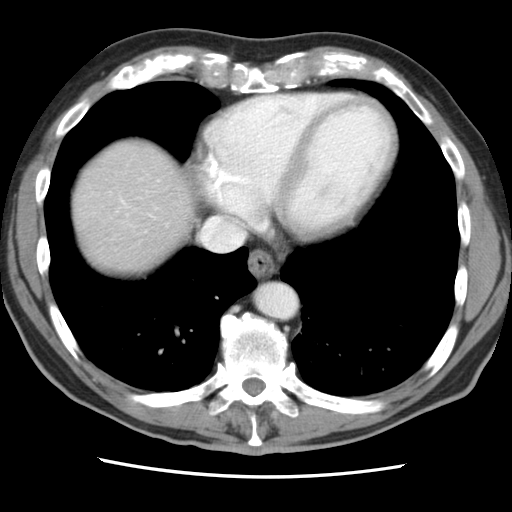
Contrast-enhanced abdominal CT, one axial slice; slice 79 of 83 in the series (ordered by position); soft-tissue window (W 400 / L 40 HU); 5 mm slice thickness; 512 × 512 image matrix, field of view 321 × 321 mm. Male patient, age 69 years. Case-level facts recorded for this patient, not image findings: diagnosis: colorectal cancer liver metastases, imaged before liver resection; multiple liver metastases: yes.
Annotated regions visible in this slice (outlined manually by an expert reader):
- hepatic veins: bounding box (x1, y1, x2, y2) in pixels: (121, 199, 245, 251)
- liver: (71, 138, 193, 272)
- planned liver remnant (the part of the liver to remain after resection): (71, 154, 195, 272)